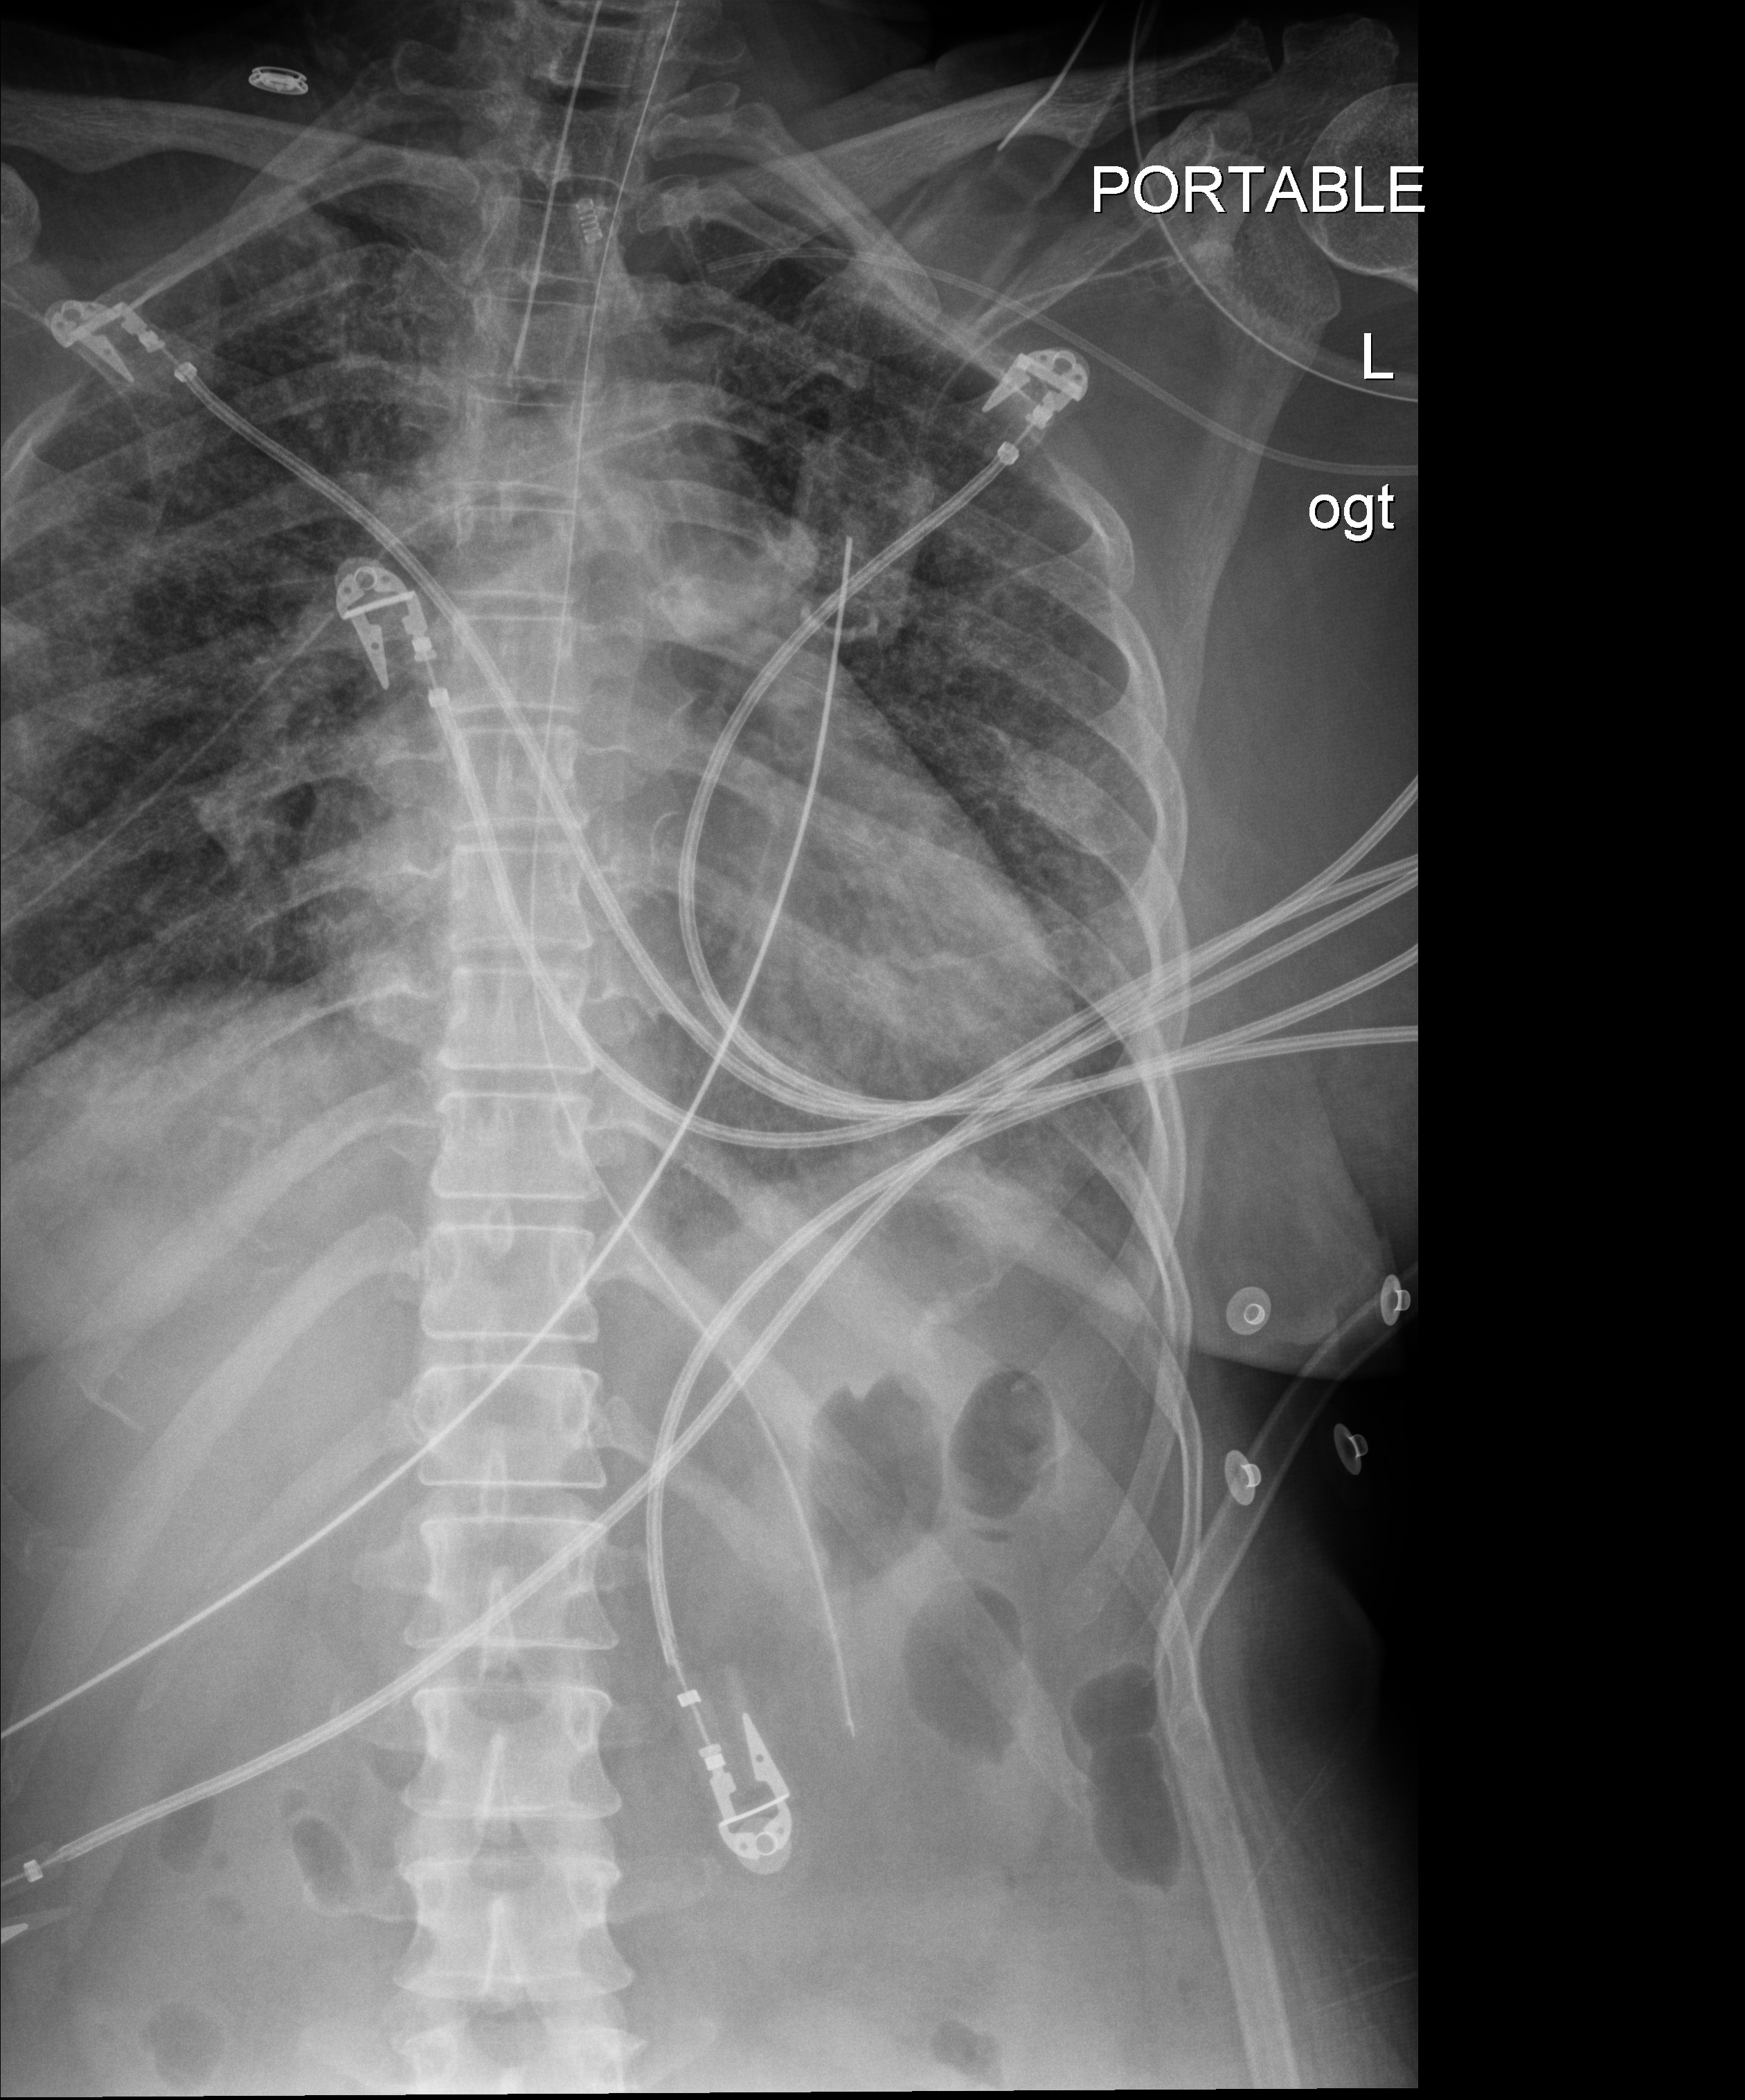
Portable chest radiograph; anteroposterior (AP) projection. Patient hospitalised with COVID-19; male, aged 18–59 years.
From the hospital-stay record, not from the radiograph (when in the stay this image was taken is not recorded): admitted to intensive care during this hospital stay: yes; chronic kidney disease (admission record): no; hypertension (admission record): yes.